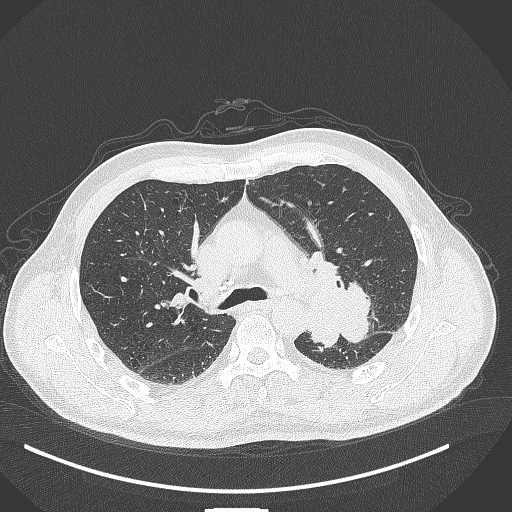
Chest CT, one axial slice. Slice 274 of 429 in the series (ordered by position). Reconstruction kernel B70f. 120 kVp. Lung window (W 1500 / L -600 HU). 1 mm slice thickness. 512 × 512 image matrix, field of view 400 × 400 mm. Patient: male, 55 years. Case-level facts recorded for this patient, not image findings: clinical TNM (as recorded): T3 N0 M1c.
Structures marked on this image (rectangle marked by the reading radiologist):
- lung tumour (recorded histology: adenocarcinoma): bounding box <301,276,373,346> (left, top, right, bottom; pixels)